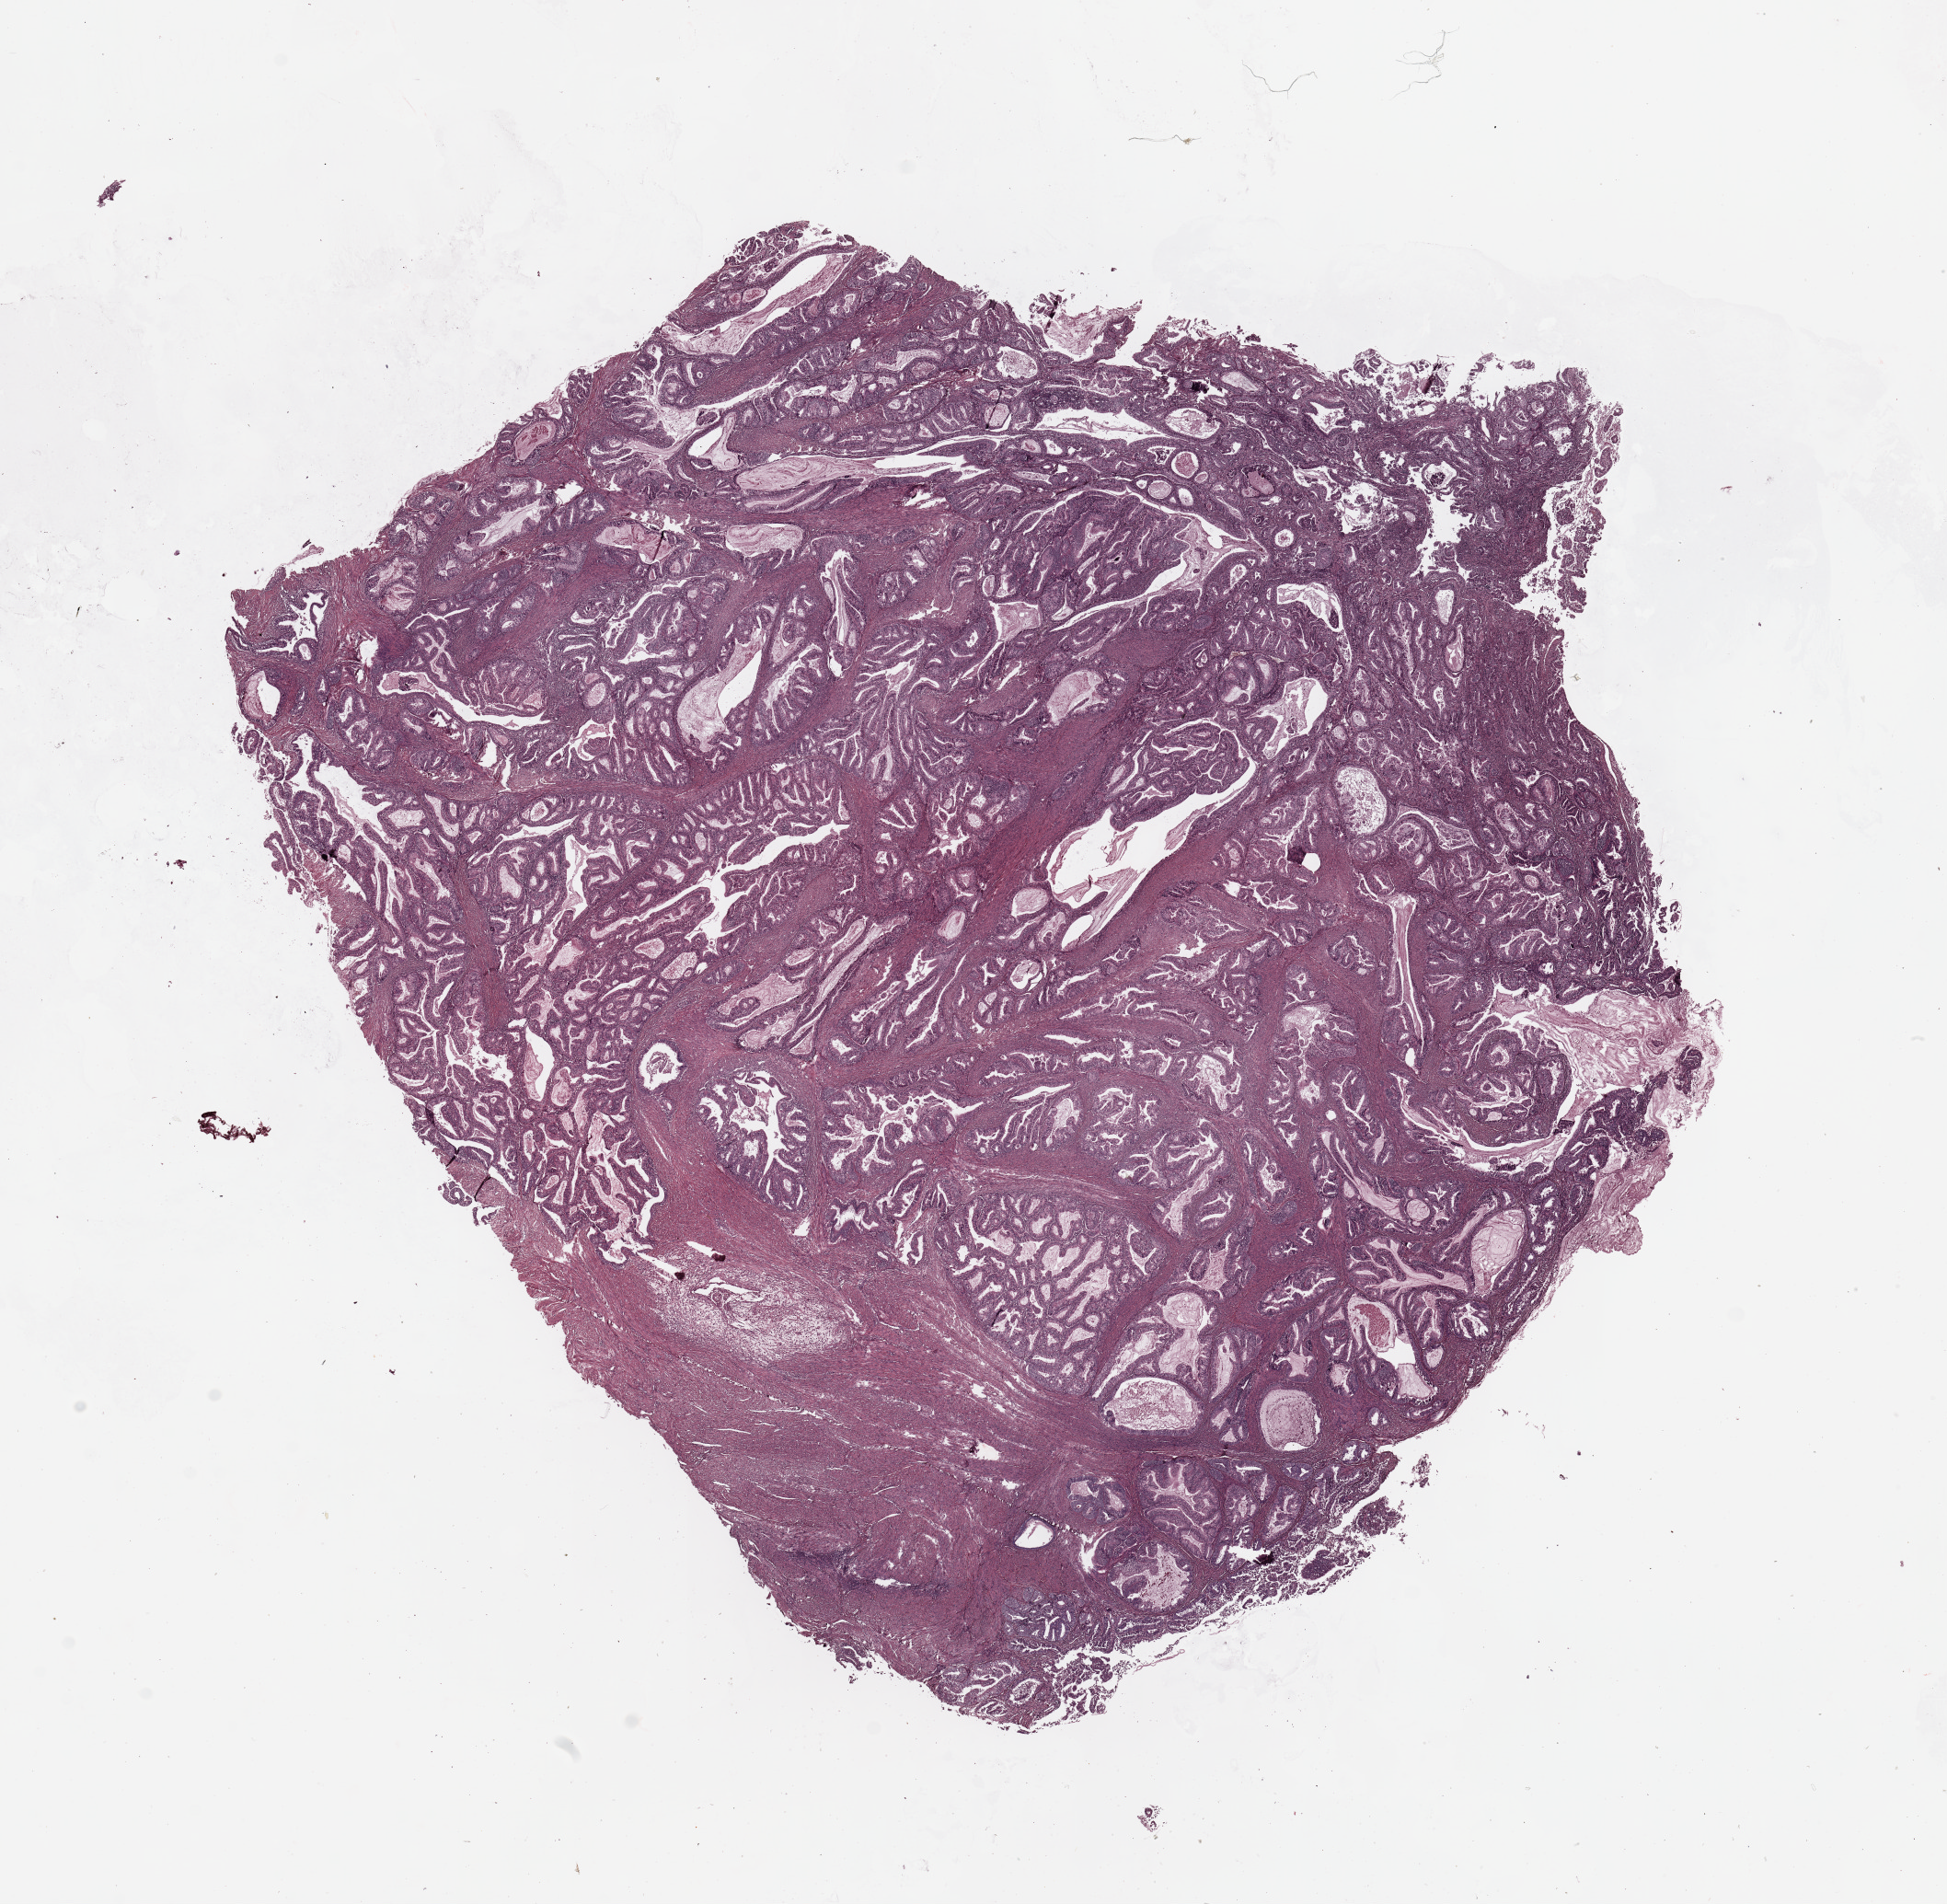
Whole-slide histology image, Hematoxylin and eosin (H&E) stained, whole scanned area (about 16.7 x 16.4 mm) shown as a low-resolution overview, tumour tissue sample, uterus. Female, 58 y/o. Histologic grade: G1 (well differentiated).
Histologic diagnosis: Endometrioid adenocarcinoma, NOS. AJCC pathologic stage: I.